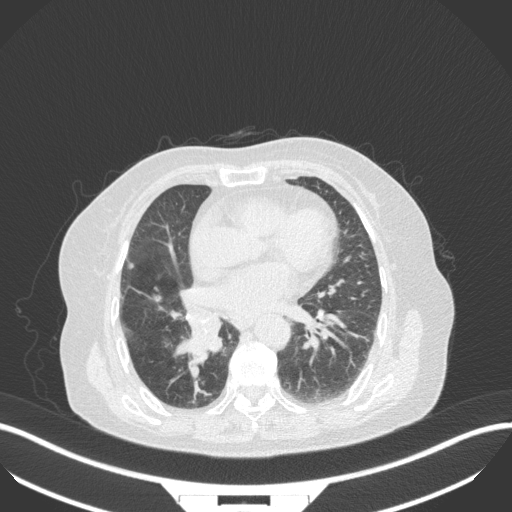
Chest CT, one axial slice; position 142 of 329 along the scan axis; reconstruction kernel B31f; 120 kVp; lung window (W 1500 / L -600 HU); 512 × 512 image matrix, field of view 400 × 400 mm. Patient: female, 75 years. Case-level facts recorded for this patient, not image findings: clinical TNM (as recorded): T1b N0 M1a; histopathological grade: G1.
Structures marked on this image (rectangle marked by the reading radiologist):
- lung tumour (recorded histology: squamous cell carcinoma): bounding box <171,310,222,362> (left, top, right, bottom; pixels)